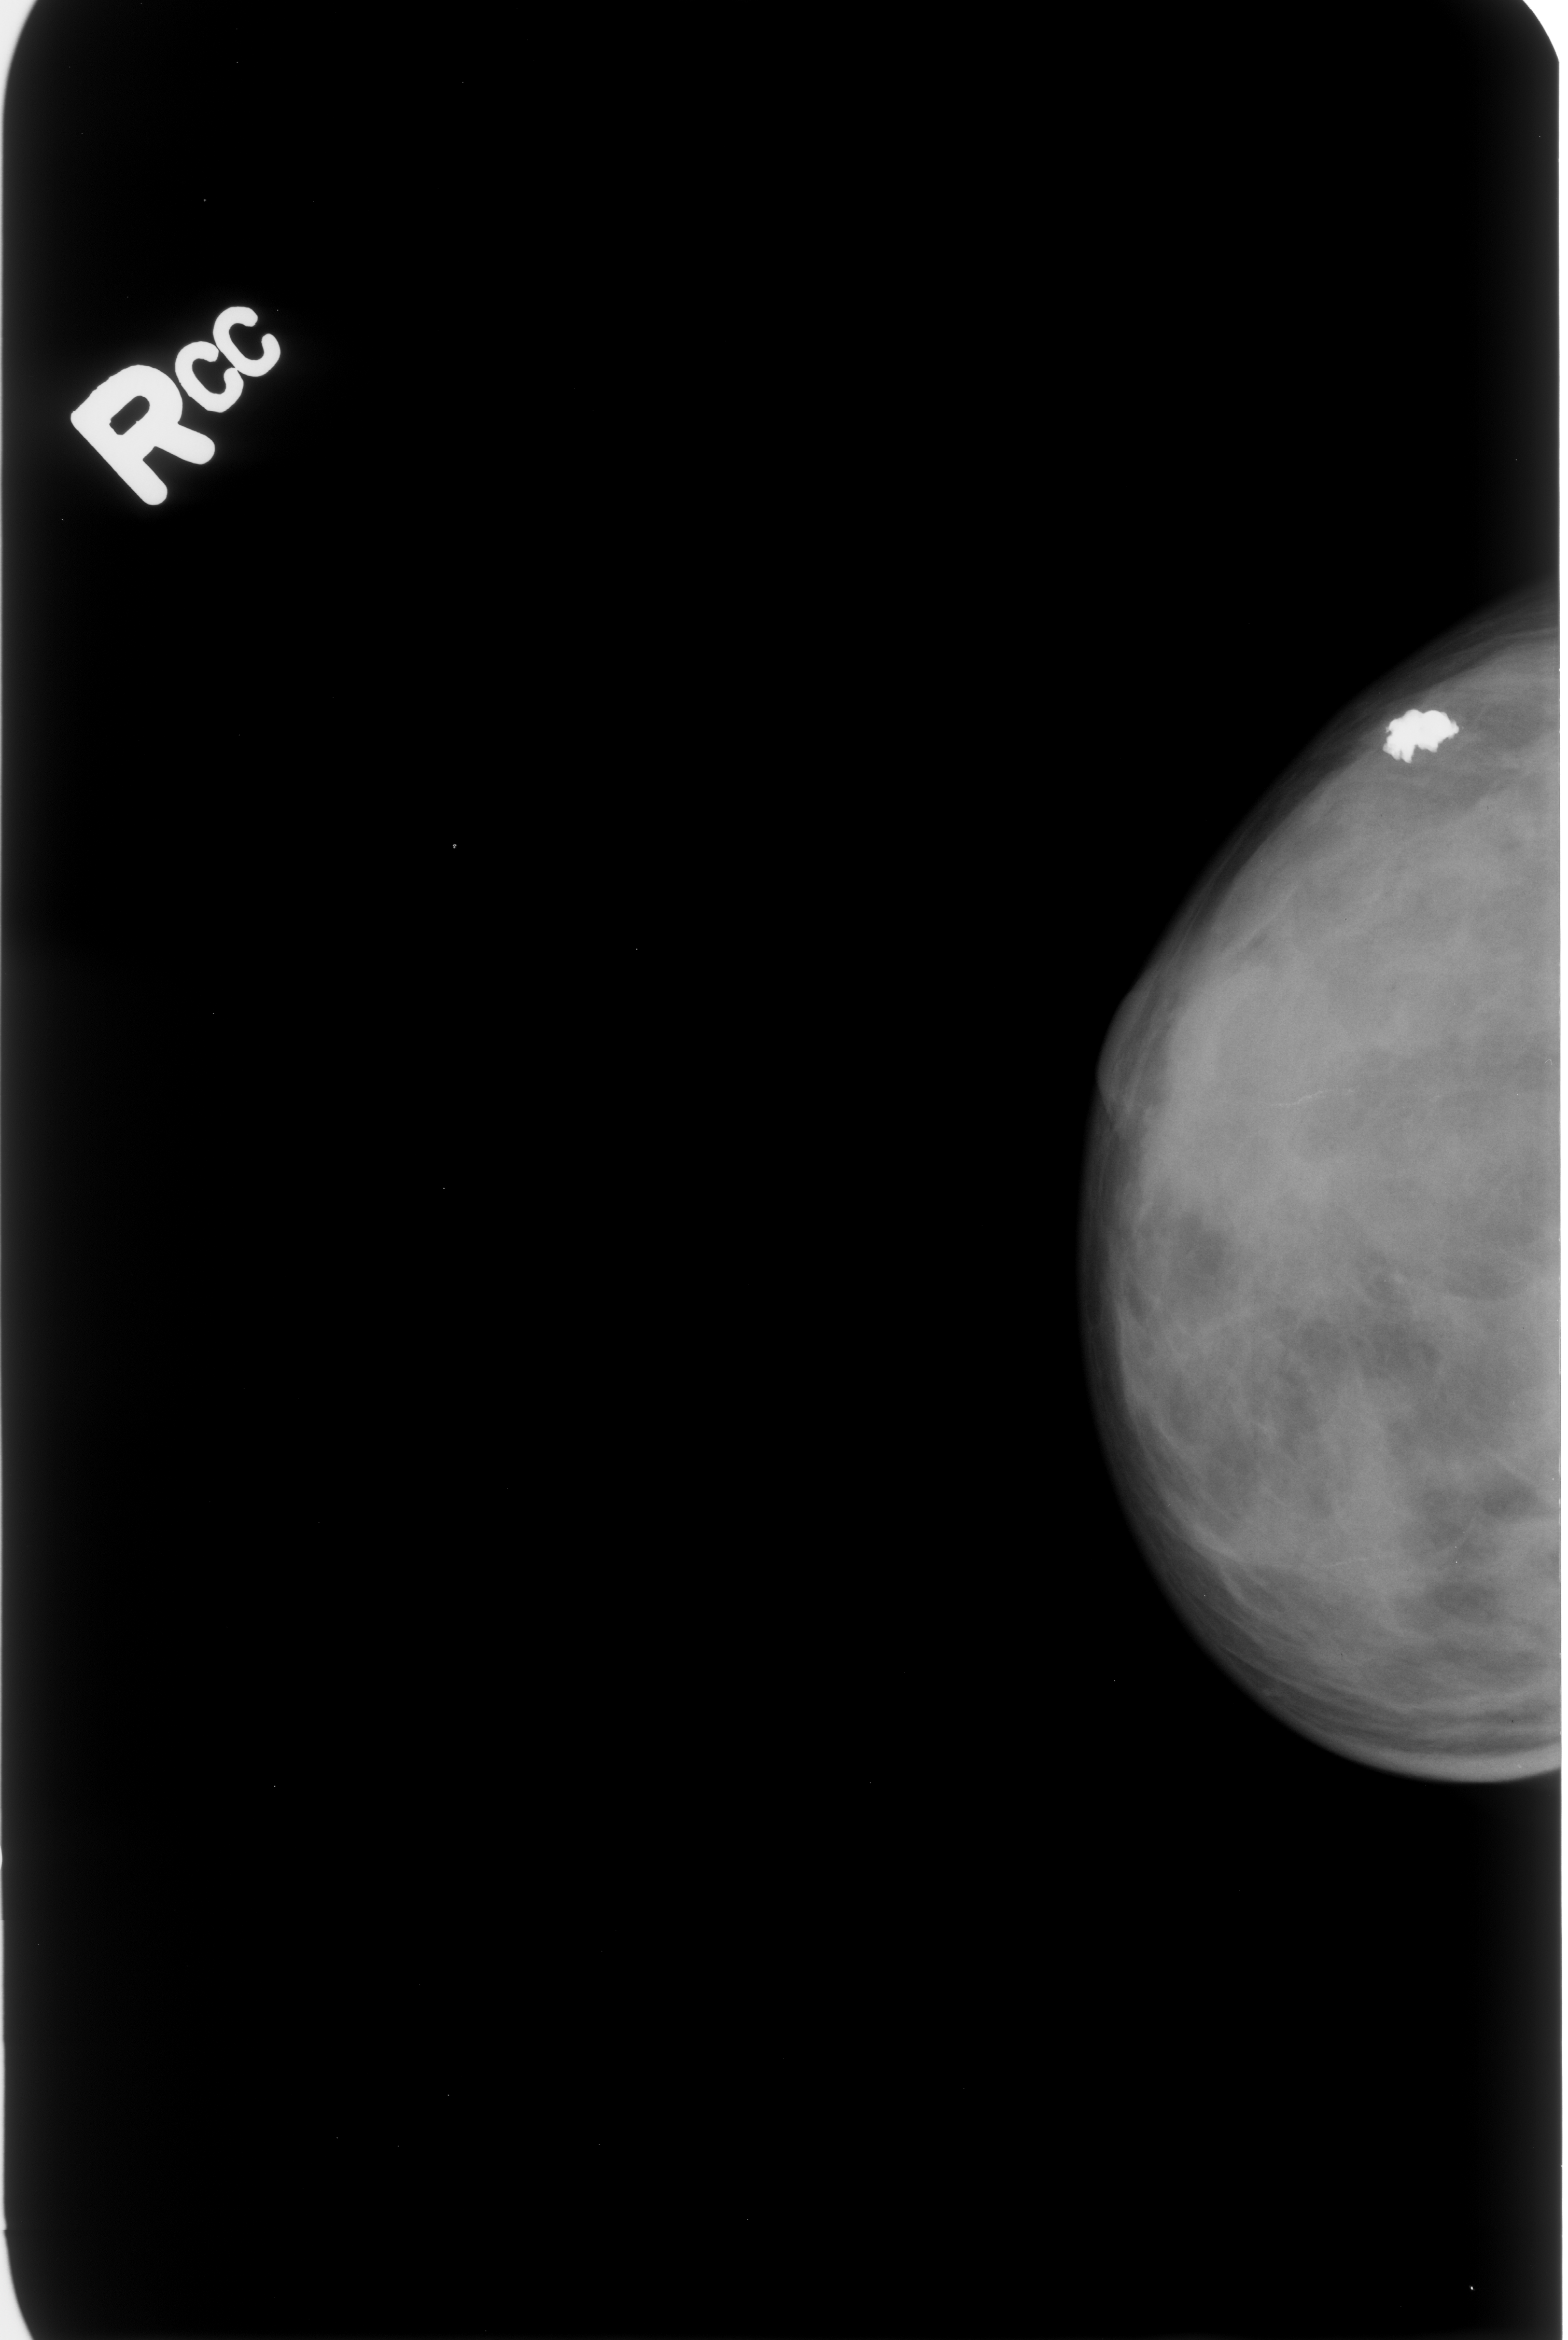
Digitized screen-film mammogram, right breast, CC view.
Marked findings (only marked abnormalities are described; nothing is implied about the rest of the image): calcifications, morphology coarse; BI-RADS assessment category 2; benign without callback (not worked up further).